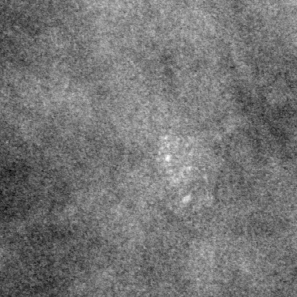
Region of interest cut from a scanned film mammogram (one marked finding), left breast, CC view.
- Finding: calcifications, morphology pleomorphic, distribution clustered; BI-RADS assessment category 4; pathology result (as recorded, not read from the image): benign.